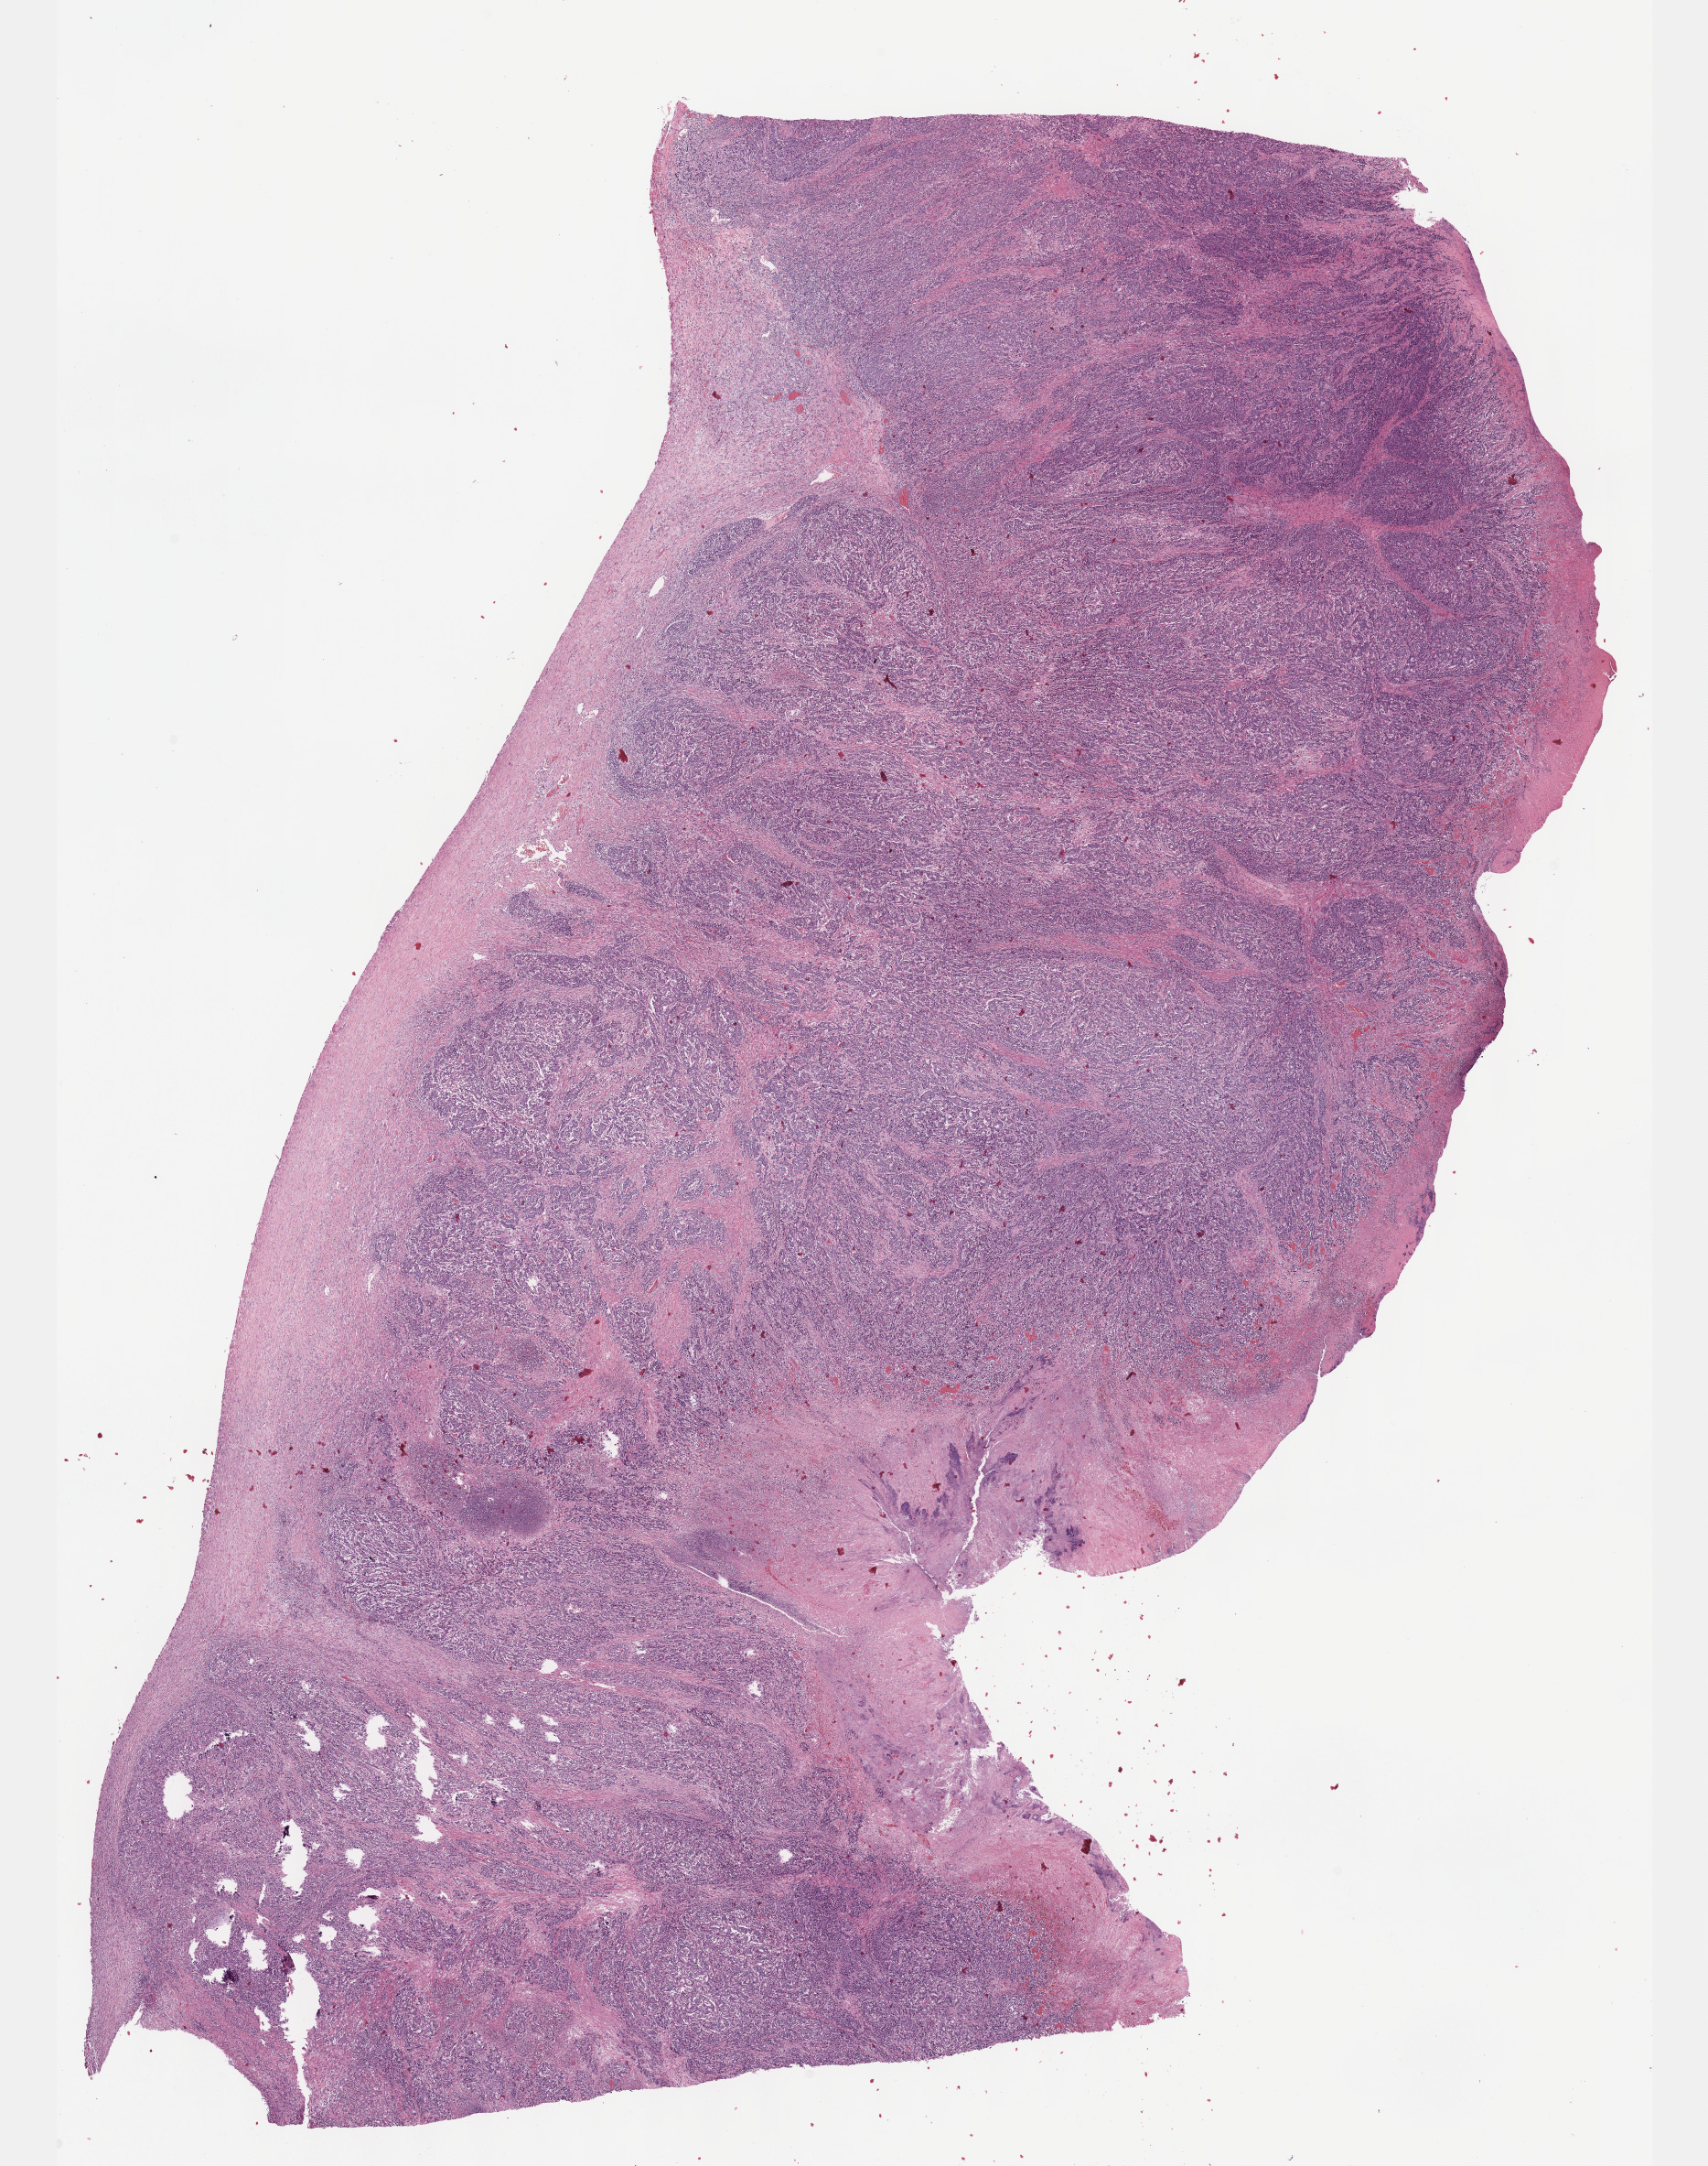
Digitized H&E-stained tissue section (whole slide), low-resolution overview of the scanned area, about 15.1 x 19.1 mm (from a 40x scan); formalin-fixed paraffin-embedded (FFPE) diagnostic section; stomach, primary tumour sample. Male, age 79 years at initial diagnosis. Histologic grade: G3 (poorly differentiated).
Diagnosis: Adenocarcinoma, NOS. Lymph nodes positive (case pathology): 0 of 20 examined. AJCC pathologic stage: IIA (7th edition).